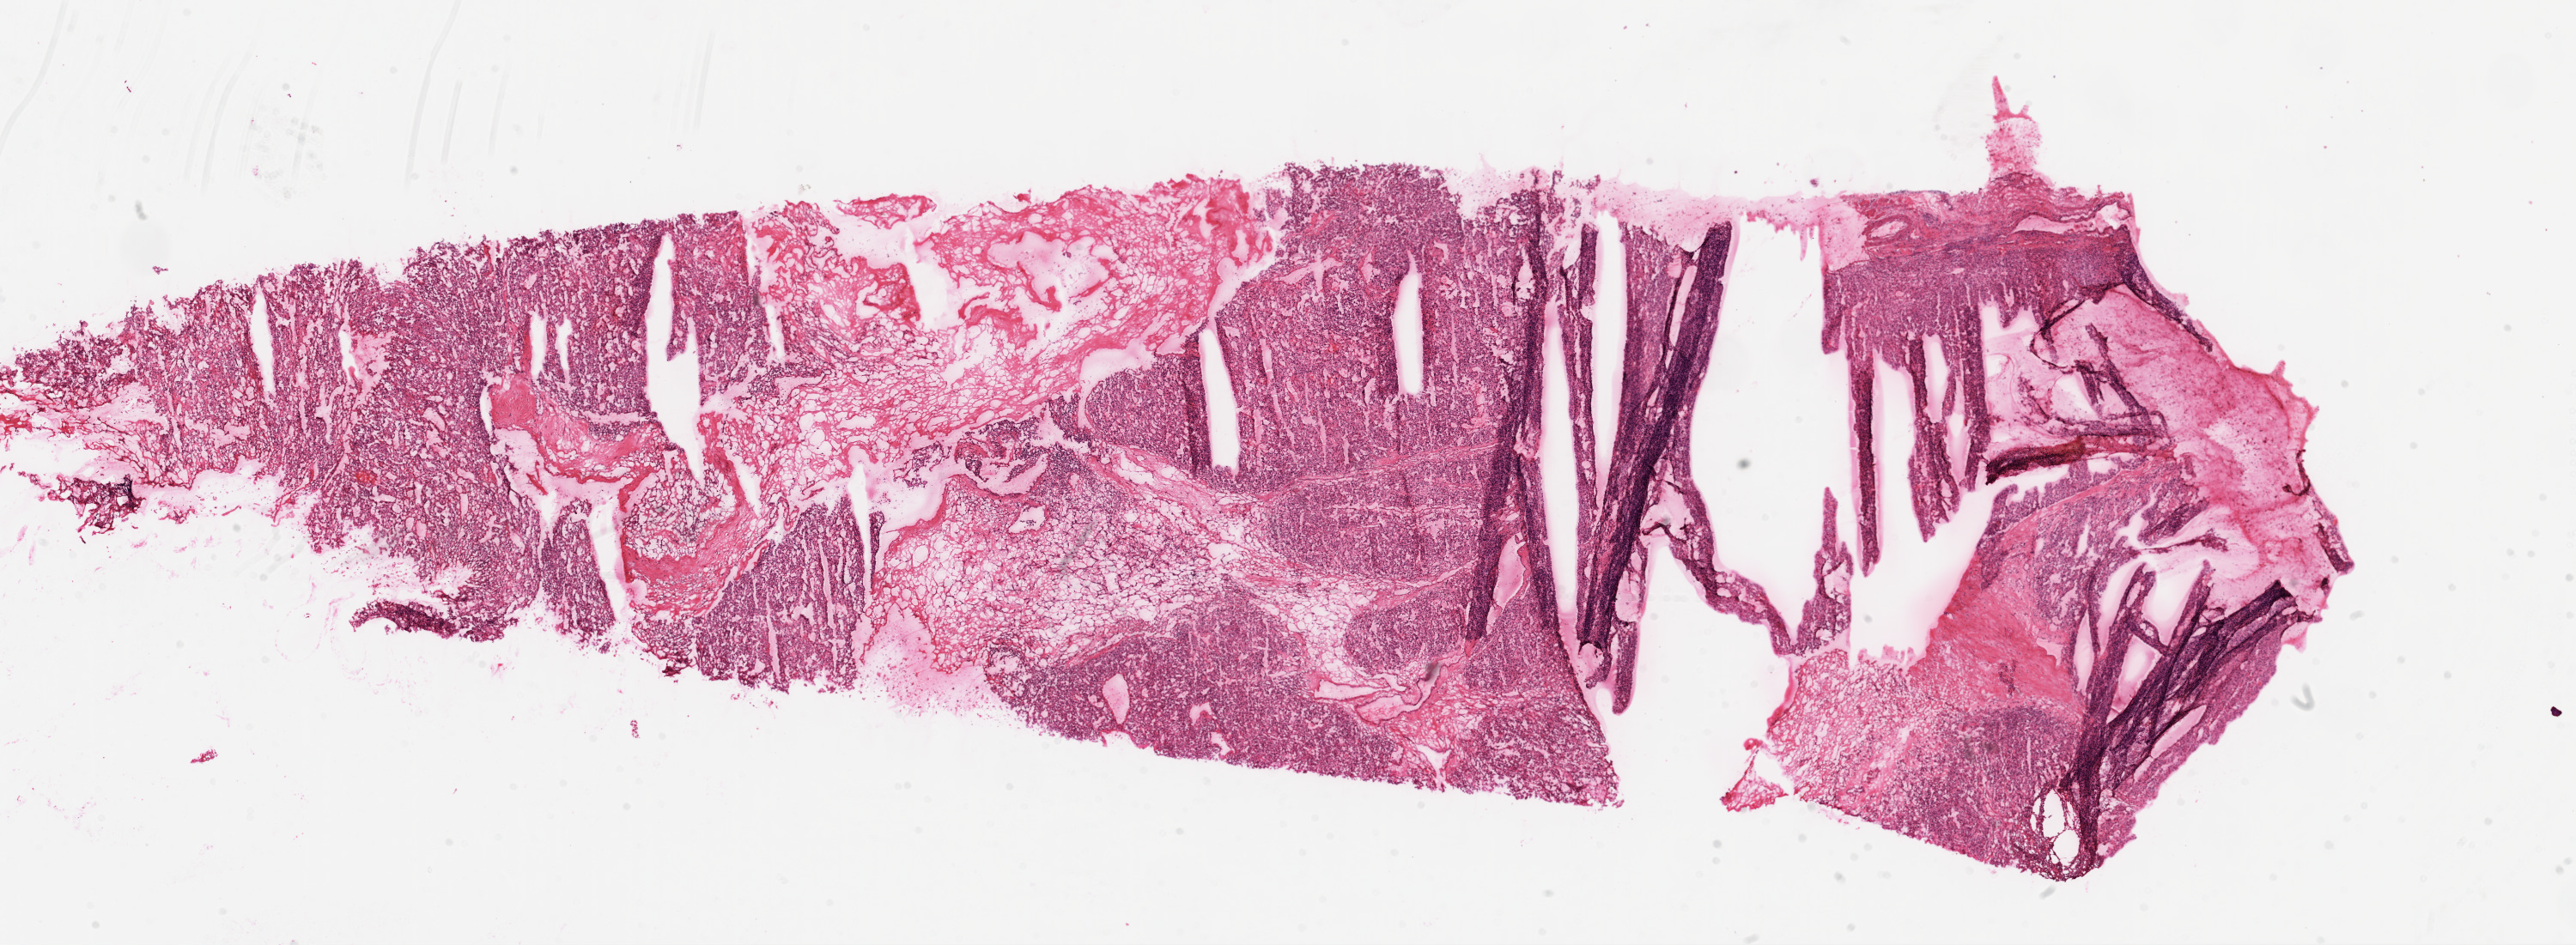
Whole-slide histology image, H&E-stained — whole scanned area (about 24.1 x 8.8 mm) shown as a low-resolution overview, frozen section from the top of the tissue portion, primary tumour sample from the kidney. Female patient; age at initial diagnosis 76 years. Histologic grade: G3 (poorly differentiated). Slide review estimates, as recorded: tumour cells 90%, tumour nuclei 85%, normal cells 0%, stromal cells 10%, necrosis 0%.
TNM: T1b NX M0. AJCC pathologic stage: I. Diagnosis: Clear cell adenocarcinoma, NOS.